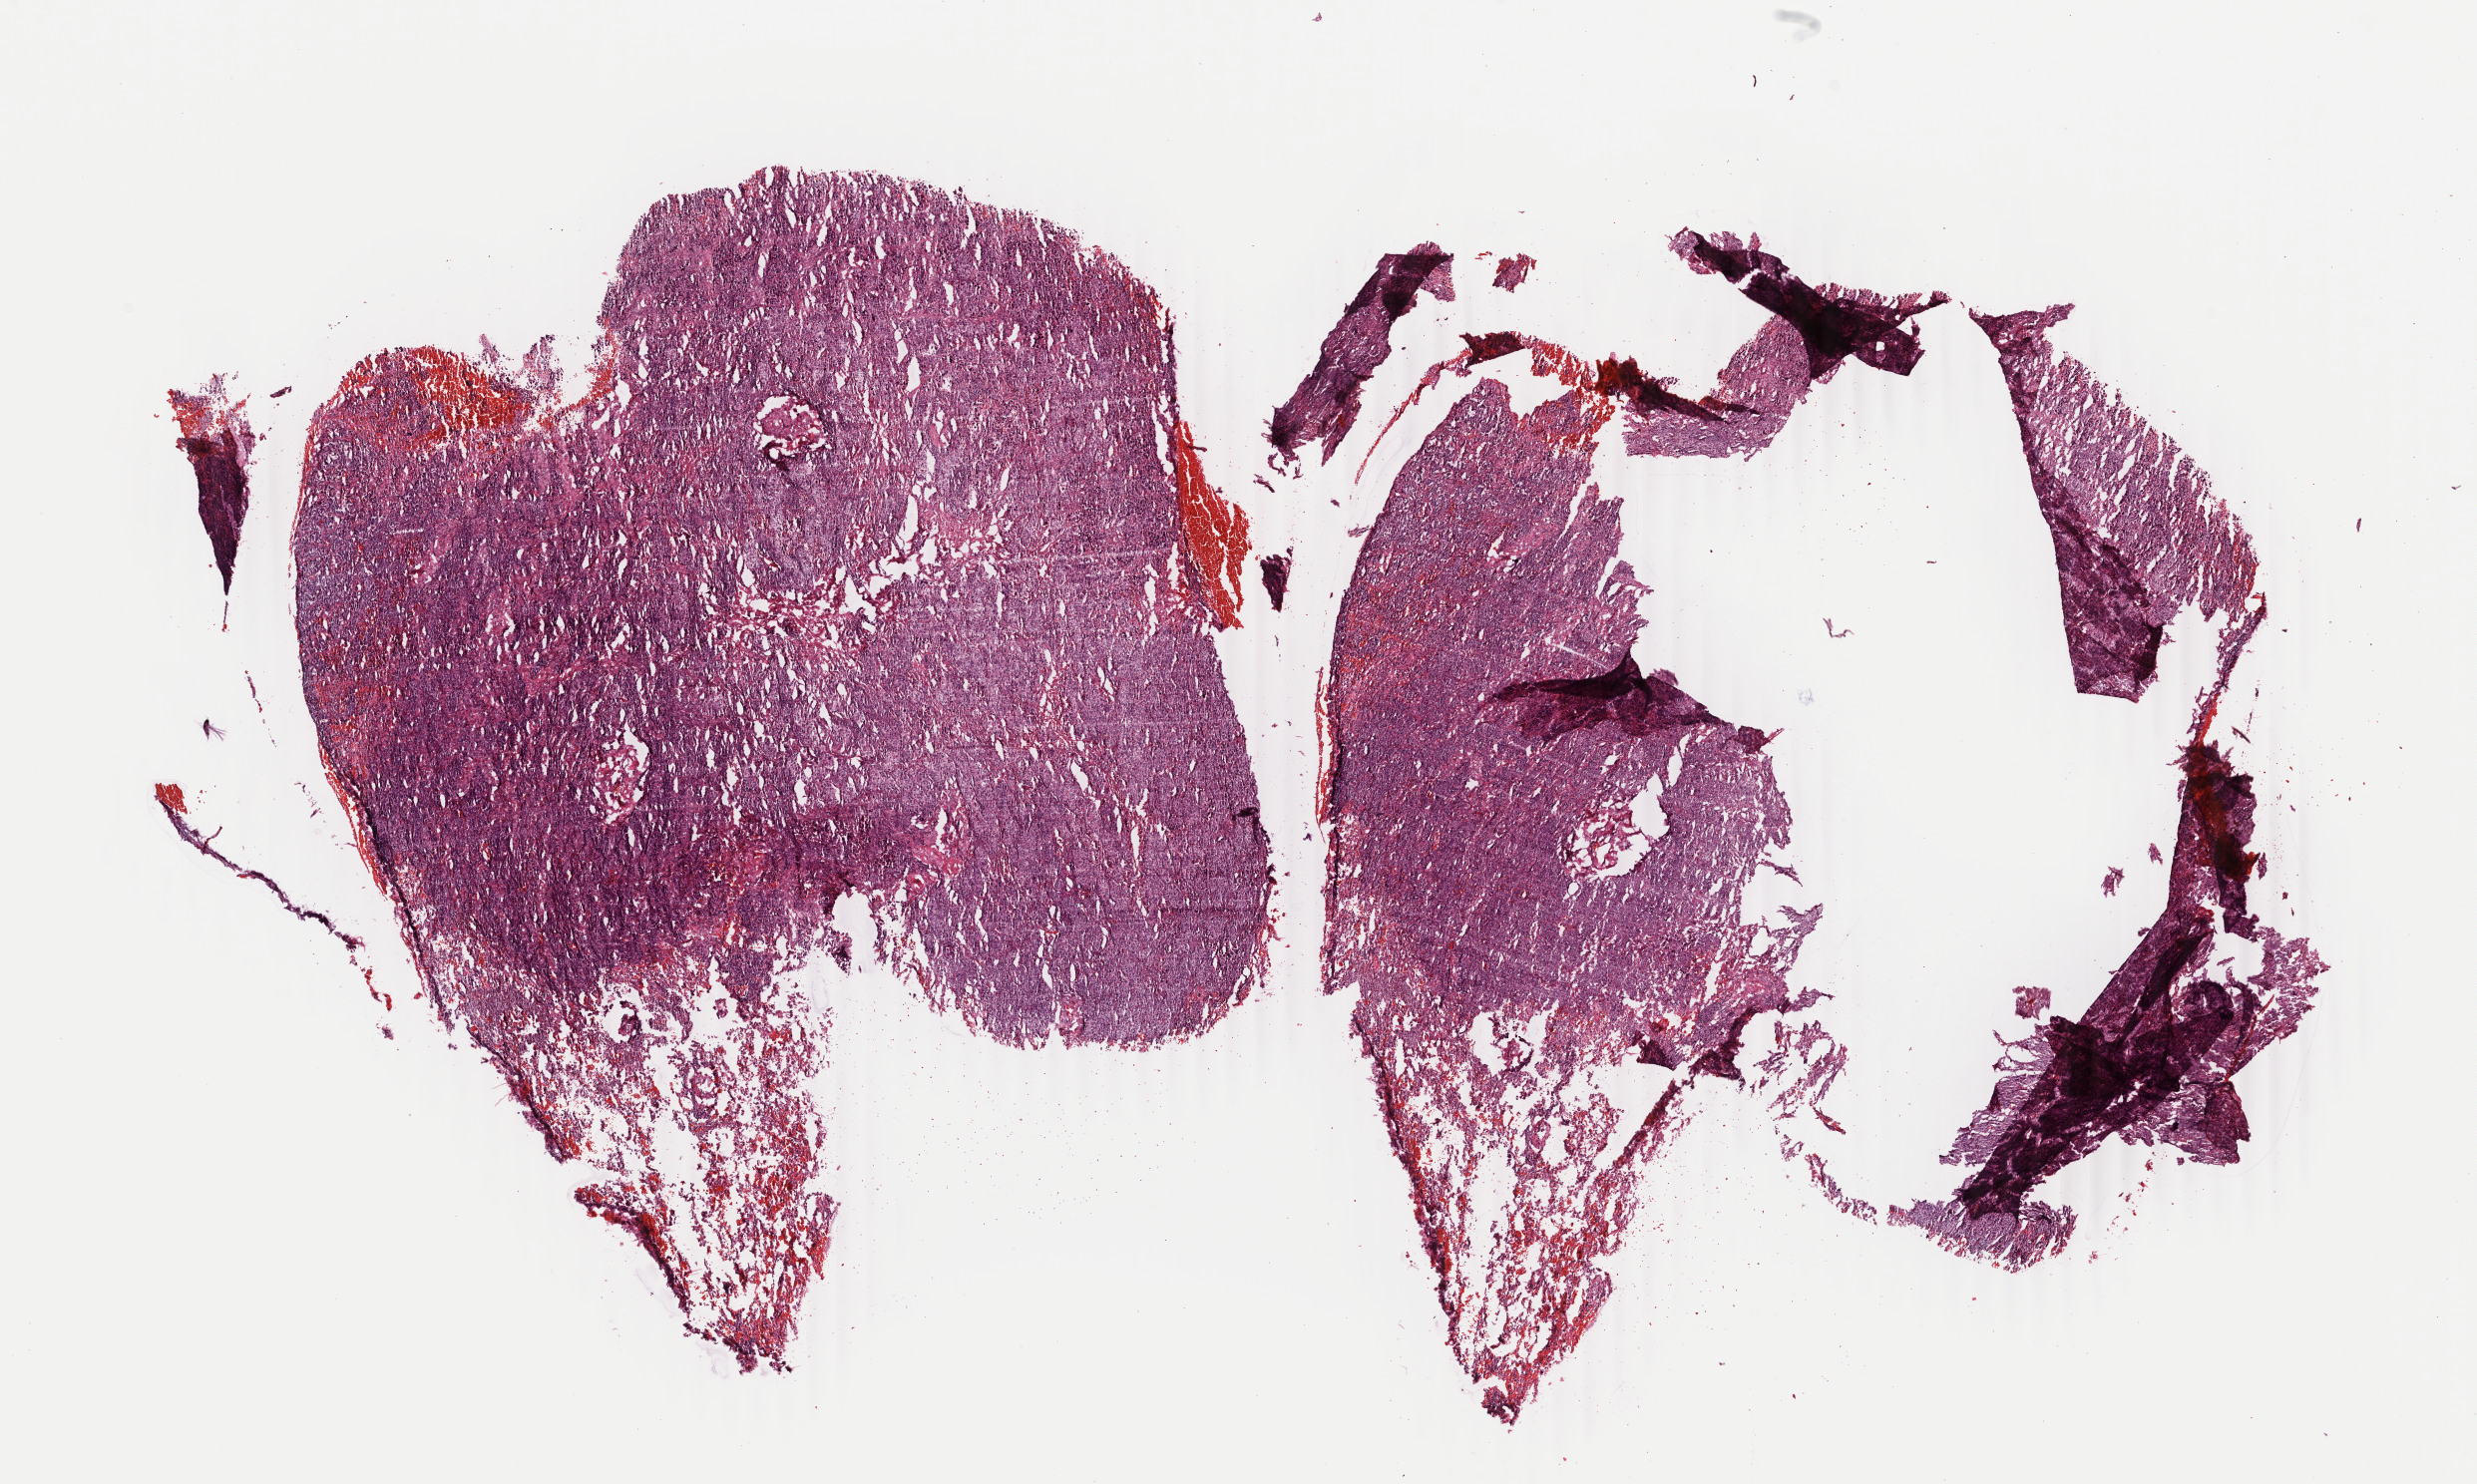
Hematoxylin and eosin (H&E) stained whole-slide image — whole scanned area (about 19.8 x 11.8 mm, acquisition: 40x scan) shown as a low-resolution overview; frozen section; sample: primary tumour, lung. Female patient; age at initial diagnosis 60 years. Slide review estimates, as recorded: tumour cells 70%, tumour nuclei 70%, normal cells 0%, stromal cells 22%, necrosis 8%. Infiltration values recorded for this section: lymphocyte infiltration 4%, monocyte infiltration 2%, neutrophil infiltration 4%.
Laterality: left. AJCC pathologic stage: IA. Diagnosis: Adenocarcinoma, NOS (upper lobe, lung).